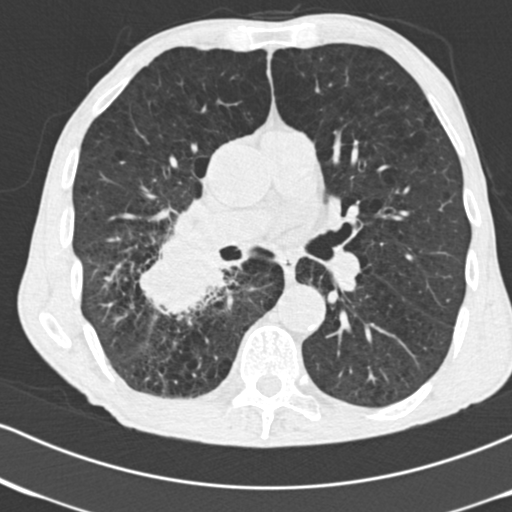
Low-dose screening chest CT, one axial slice. Position 92 of 182 along the scan axis. Reconstruction kernel B30f. 120 kVp. Lung window (W 1500 / L -600 HU). 512 × 512 image matrix, field of view 316 × 316 mm.
Structures marked on this image (outlined manually by an expert reader):
- lesion 1 (tumor, lower lobe of right lung): bounding box (x1, y1, x2, y2) in pixels: (140, 217, 225, 314)